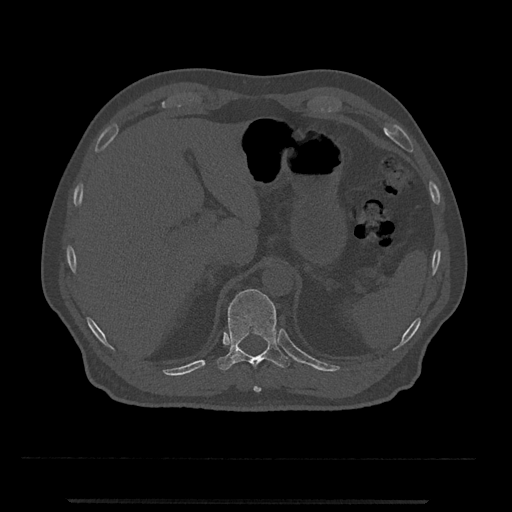
CT including the spine, one axial slice; slice 470 of 797 in the series (ordered by position); reconstruction kernel Br40s/3; 120 kVp; bone window (W 1800 / L 400 HU); 0.5 mm slice thickness; 512 × 512 image matrix. Male patient, age 63 years. Case-level facts recorded for this patient, not image findings: primary cancer: prostate.
Outlined on this slice (semi-automatically segmented with operator editing):
- T10 vertebra: box from (x=253, y=385) to (x=262, y=392) px
- T11 vertebra: (x=217, y=289)–(x=290, y=371)